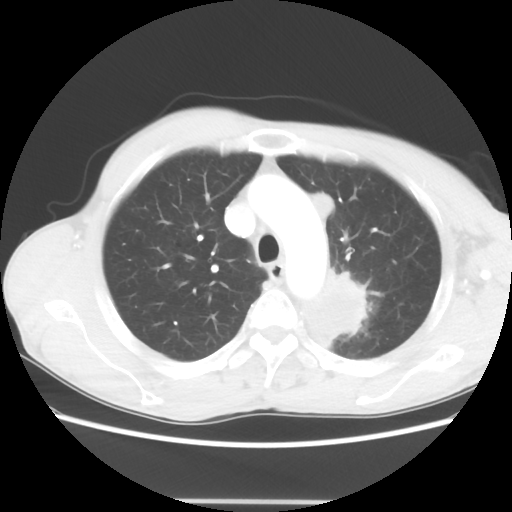
Chest CT, one axial slice; position 49 of 62 along the scan axis; reconstruction kernel STANDARD; 100 kVp; lung window (W 1500 / L -600 HU); 512 × 512 image matrix. Patient: male, 61 years. Case-level facts recorded for this patient, not image findings: clinical TNM (as recorded): T3 N1 M1.
Structures marked on this image (rectangle marked by the reading radiologist):
- lung tumour (recorded histology: adenocarcinoma): box from (x=296, y=262) to (x=372, y=356) px
- lung tumour (recorded histology: adenocarcinoma): (x=312, y=192)–(x=343, y=223)